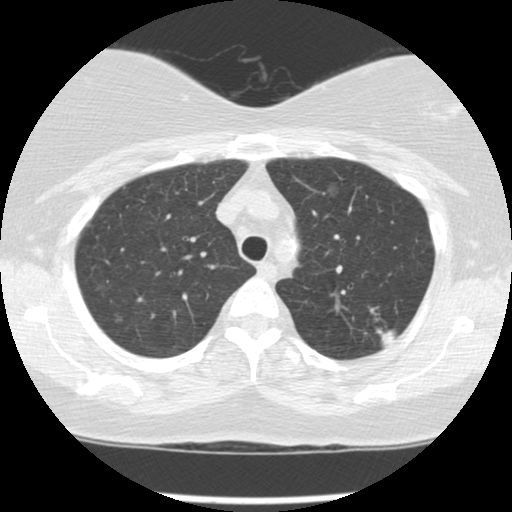
Low-dose screening chest CT, one axial slice. Slice 103 of 127 in the series (ordered by position). Reconstruction kernel STANDARD. 120 kVp. Lung window (W 1500 / L -600 HU). 2.5 mm slice thickness. 512 × 512 image matrix, field of view 310 × 310 mm.
Annotated regions visible in this slice (manually delineated by an expert):
- lesion 1 (tumor, upper lobe of left lung): box from (x=375, y=327) to (x=396, y=346) px